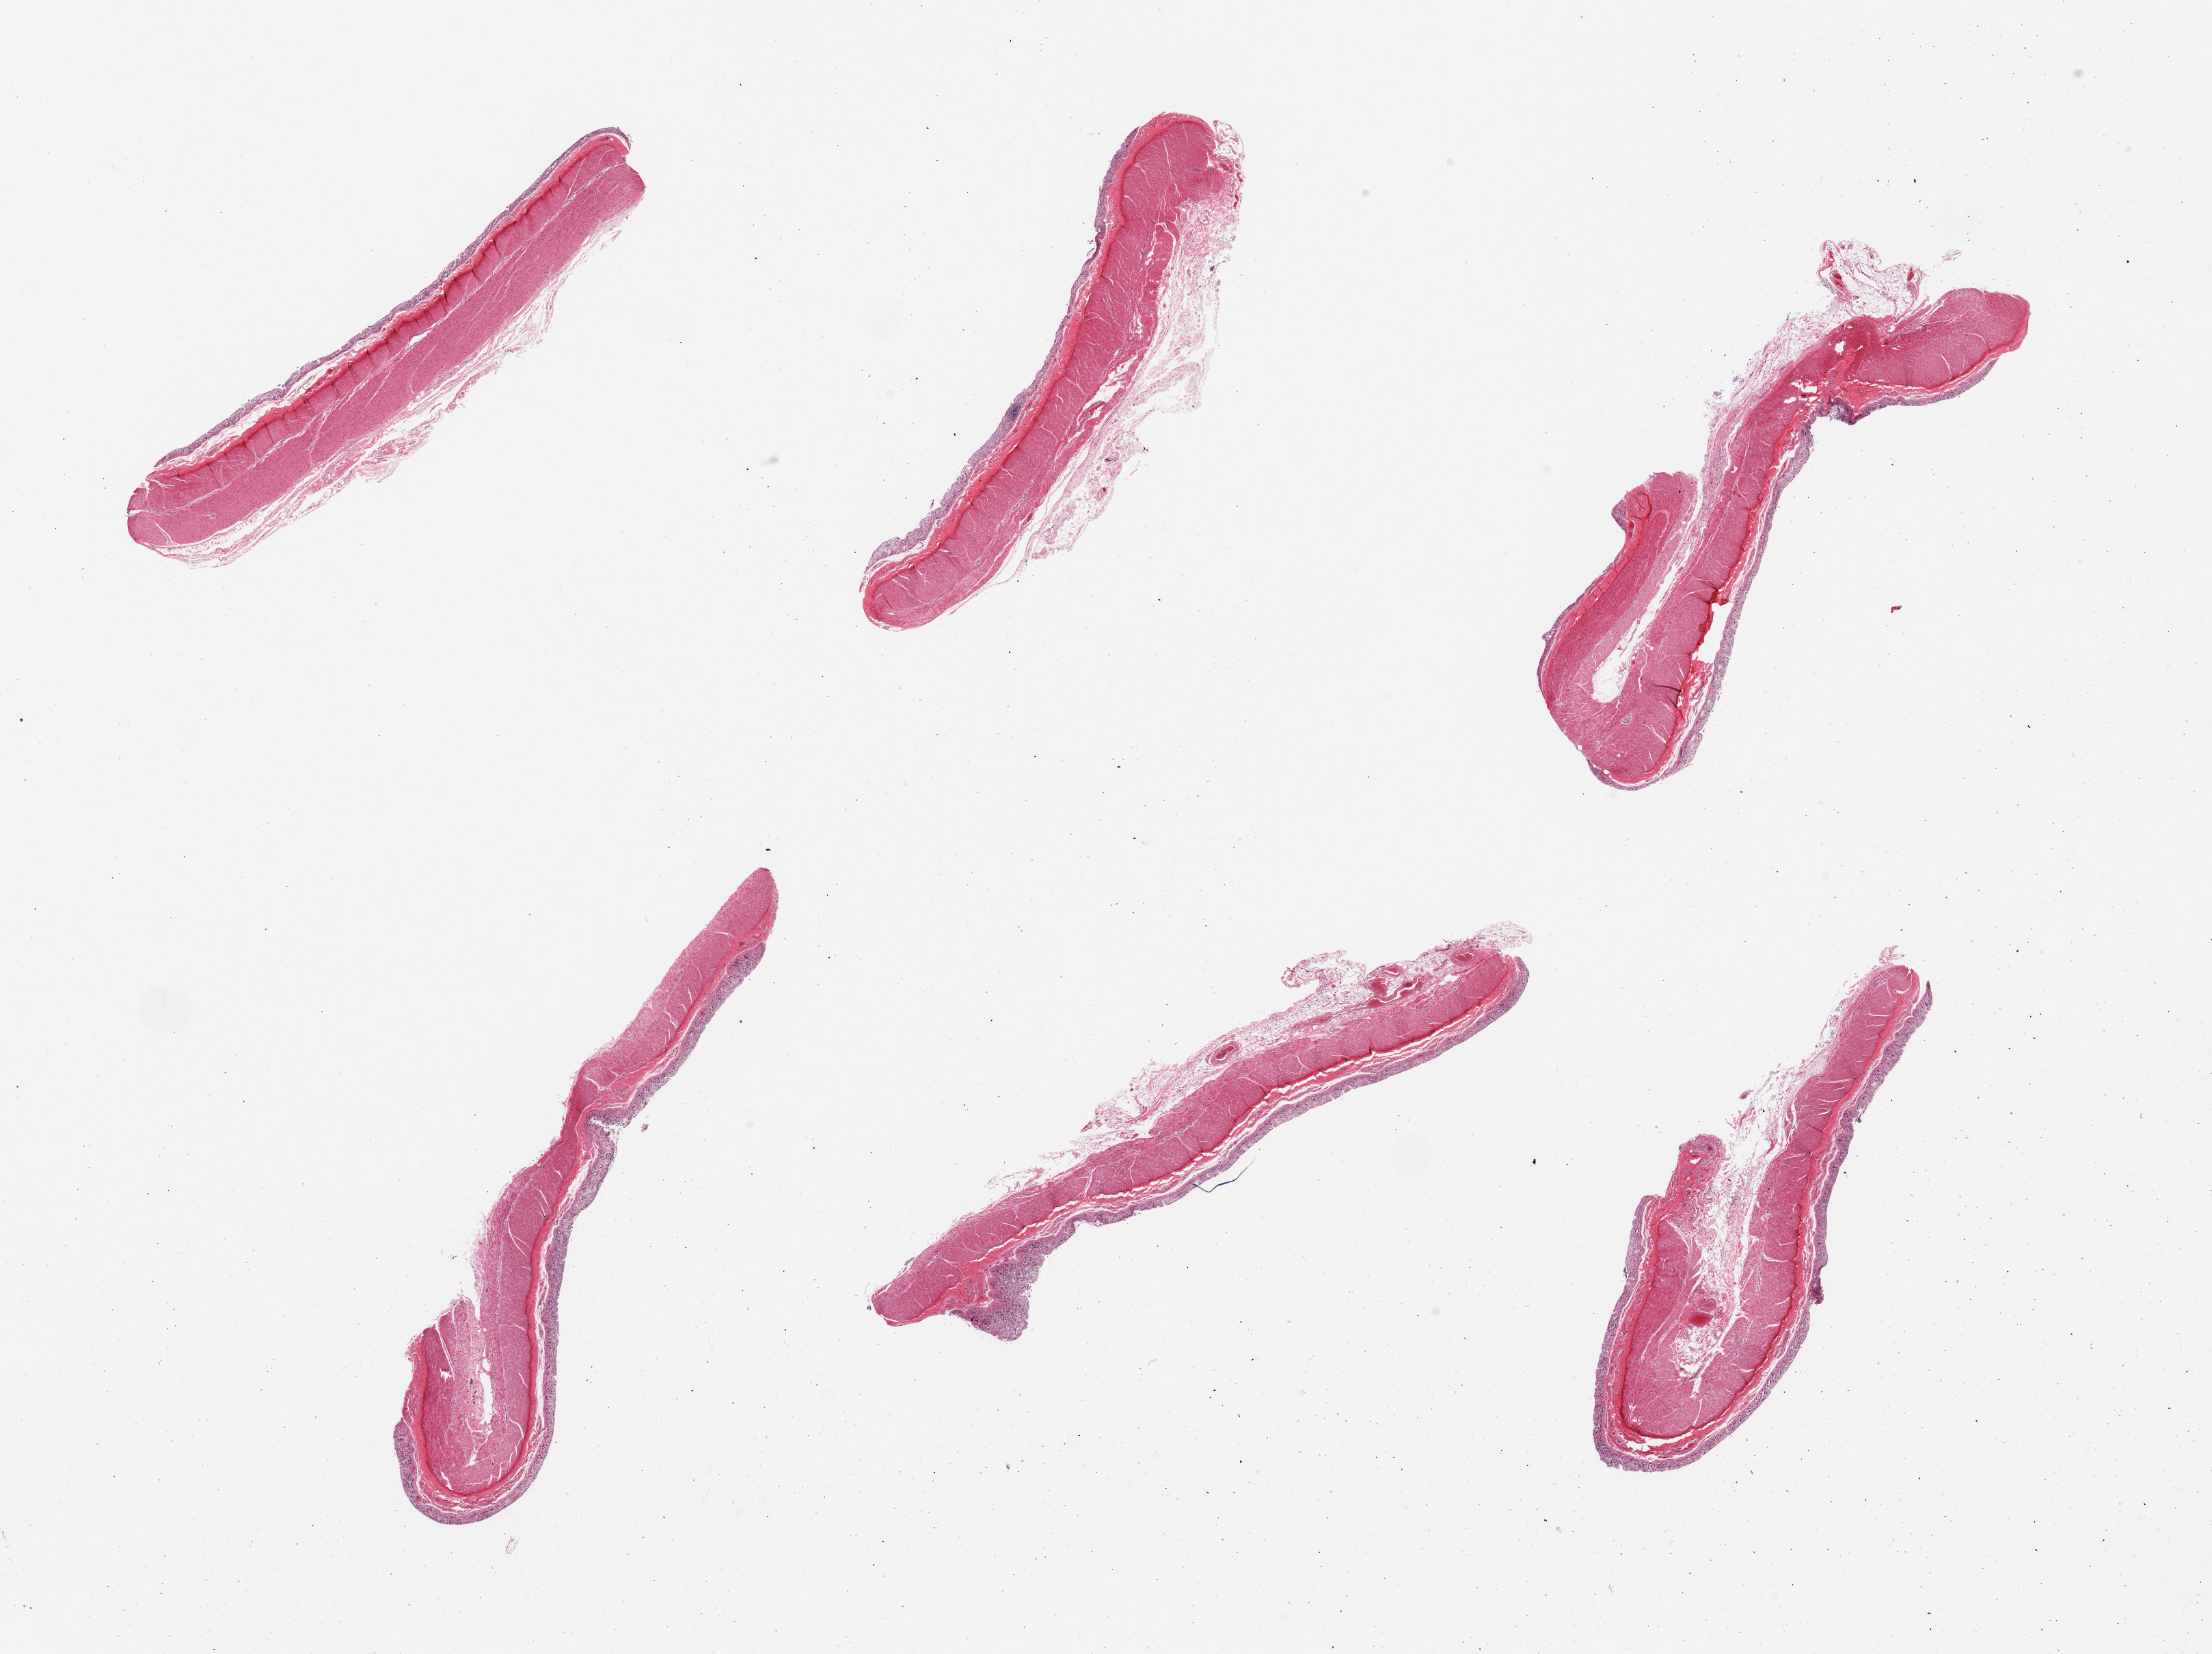
Whole-slide image, hematoxylin and eosin (H&E) stain, brightfield, low-resolution overview of the scanned area, about 25.6 x 19.1 mm. PAXgene-fixed, paraffin-embedded tissue. Section of transverse colon (target tissue). Donor tissue sample.
Reviewer comment on this tissue sample: 6 pieces; epithelium autolyzed; muscle intact.